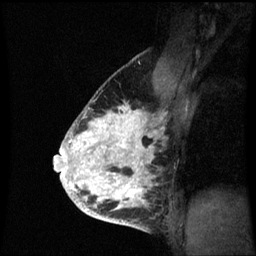
Breast MRI (dynamic contrast-enhanced), one sagittal slice. Position 44 of 60 along the scan axis. Dynamic contrast-enhanced series, image 2 of 3 at this slice position (ordered by acquisition). 1.5 T. TE 4.2 ms, TR 8.9 ms. 256 × 256 image matrix. Patient: female, 35 years. From the clinical record (not read from this slice): setting: breast cancer imaged before/during neoadjuvant chemotherapy; receptor status: HR-positive, HER2-negative.
Structures marked on this image (semi-automatic segmentation, software-assisted and operator-edited):
- analysis volume of interest (the breast-tissue region the enhancement analysis was run in; not a lesion): bounding box <66,100,162,215> (left, top, right, bottom; pixels)
- tumour enhancement mask (voxels above the 70 % enhancement threshold inside the analysis volume of interest): <66,104,157,213>